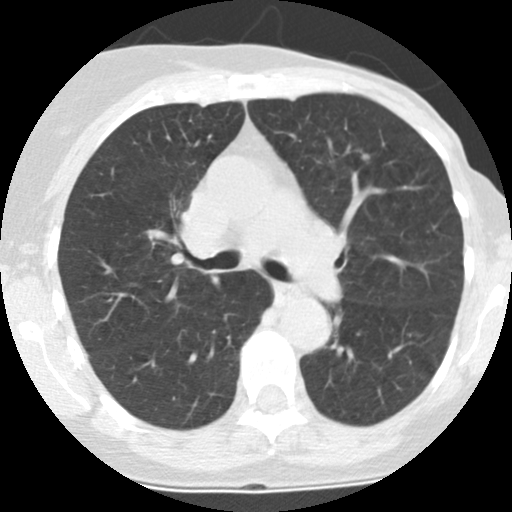
Axial slice from a low-dose chest CT screening exam. First (baseline) screen. Lung window (W 1500 / L -600 HU). Female, age 66 years at enrolment. Former smoker at enrolment.
Expert-annotated lung lesion, bounding box <358,147,374,167> (left, top, right, bottom; pixels). No non-calcified nodule or mass ≥4 mm was recorded by the screening reader at this exam. Later outcome: lung cancer diagnosed 583 days after this screen (after the second annual screen) — adenocarcinoma, NOS, left lower lobe, poorly differentiated (G3), stage IA (AJCC 6th edition), 8 mm at pathology.